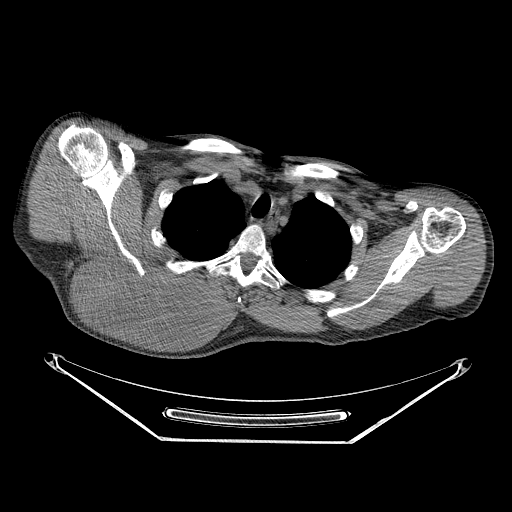
CT of an extremity soft-tissue mass (from a PET/CT study), one axial slice. Slice 197 of 267 in the series (ordered by position). Reconstruction kernel STANDARD. 140 kVp. Soft-tissue window (W 400 / L 40 HU). 512 × 512 image matrix, field of view 500 × 500 mm. Male patient. From the clinical record (not read from this slice): histological type: pleiomorphic spindle cell undifferentiated; grade: high; site of the primary tumour: right parascapusular.
Outlined on this slice (expert contour drawn on MRI and transferred to this co-registered scan by the dataset authors):
- gross tumour volume including surrounding oedema: bounding box <77,256,234,337> (left, top, right, bottom; pixels)
- gross tumour volume (mass): <77,256,220,334>